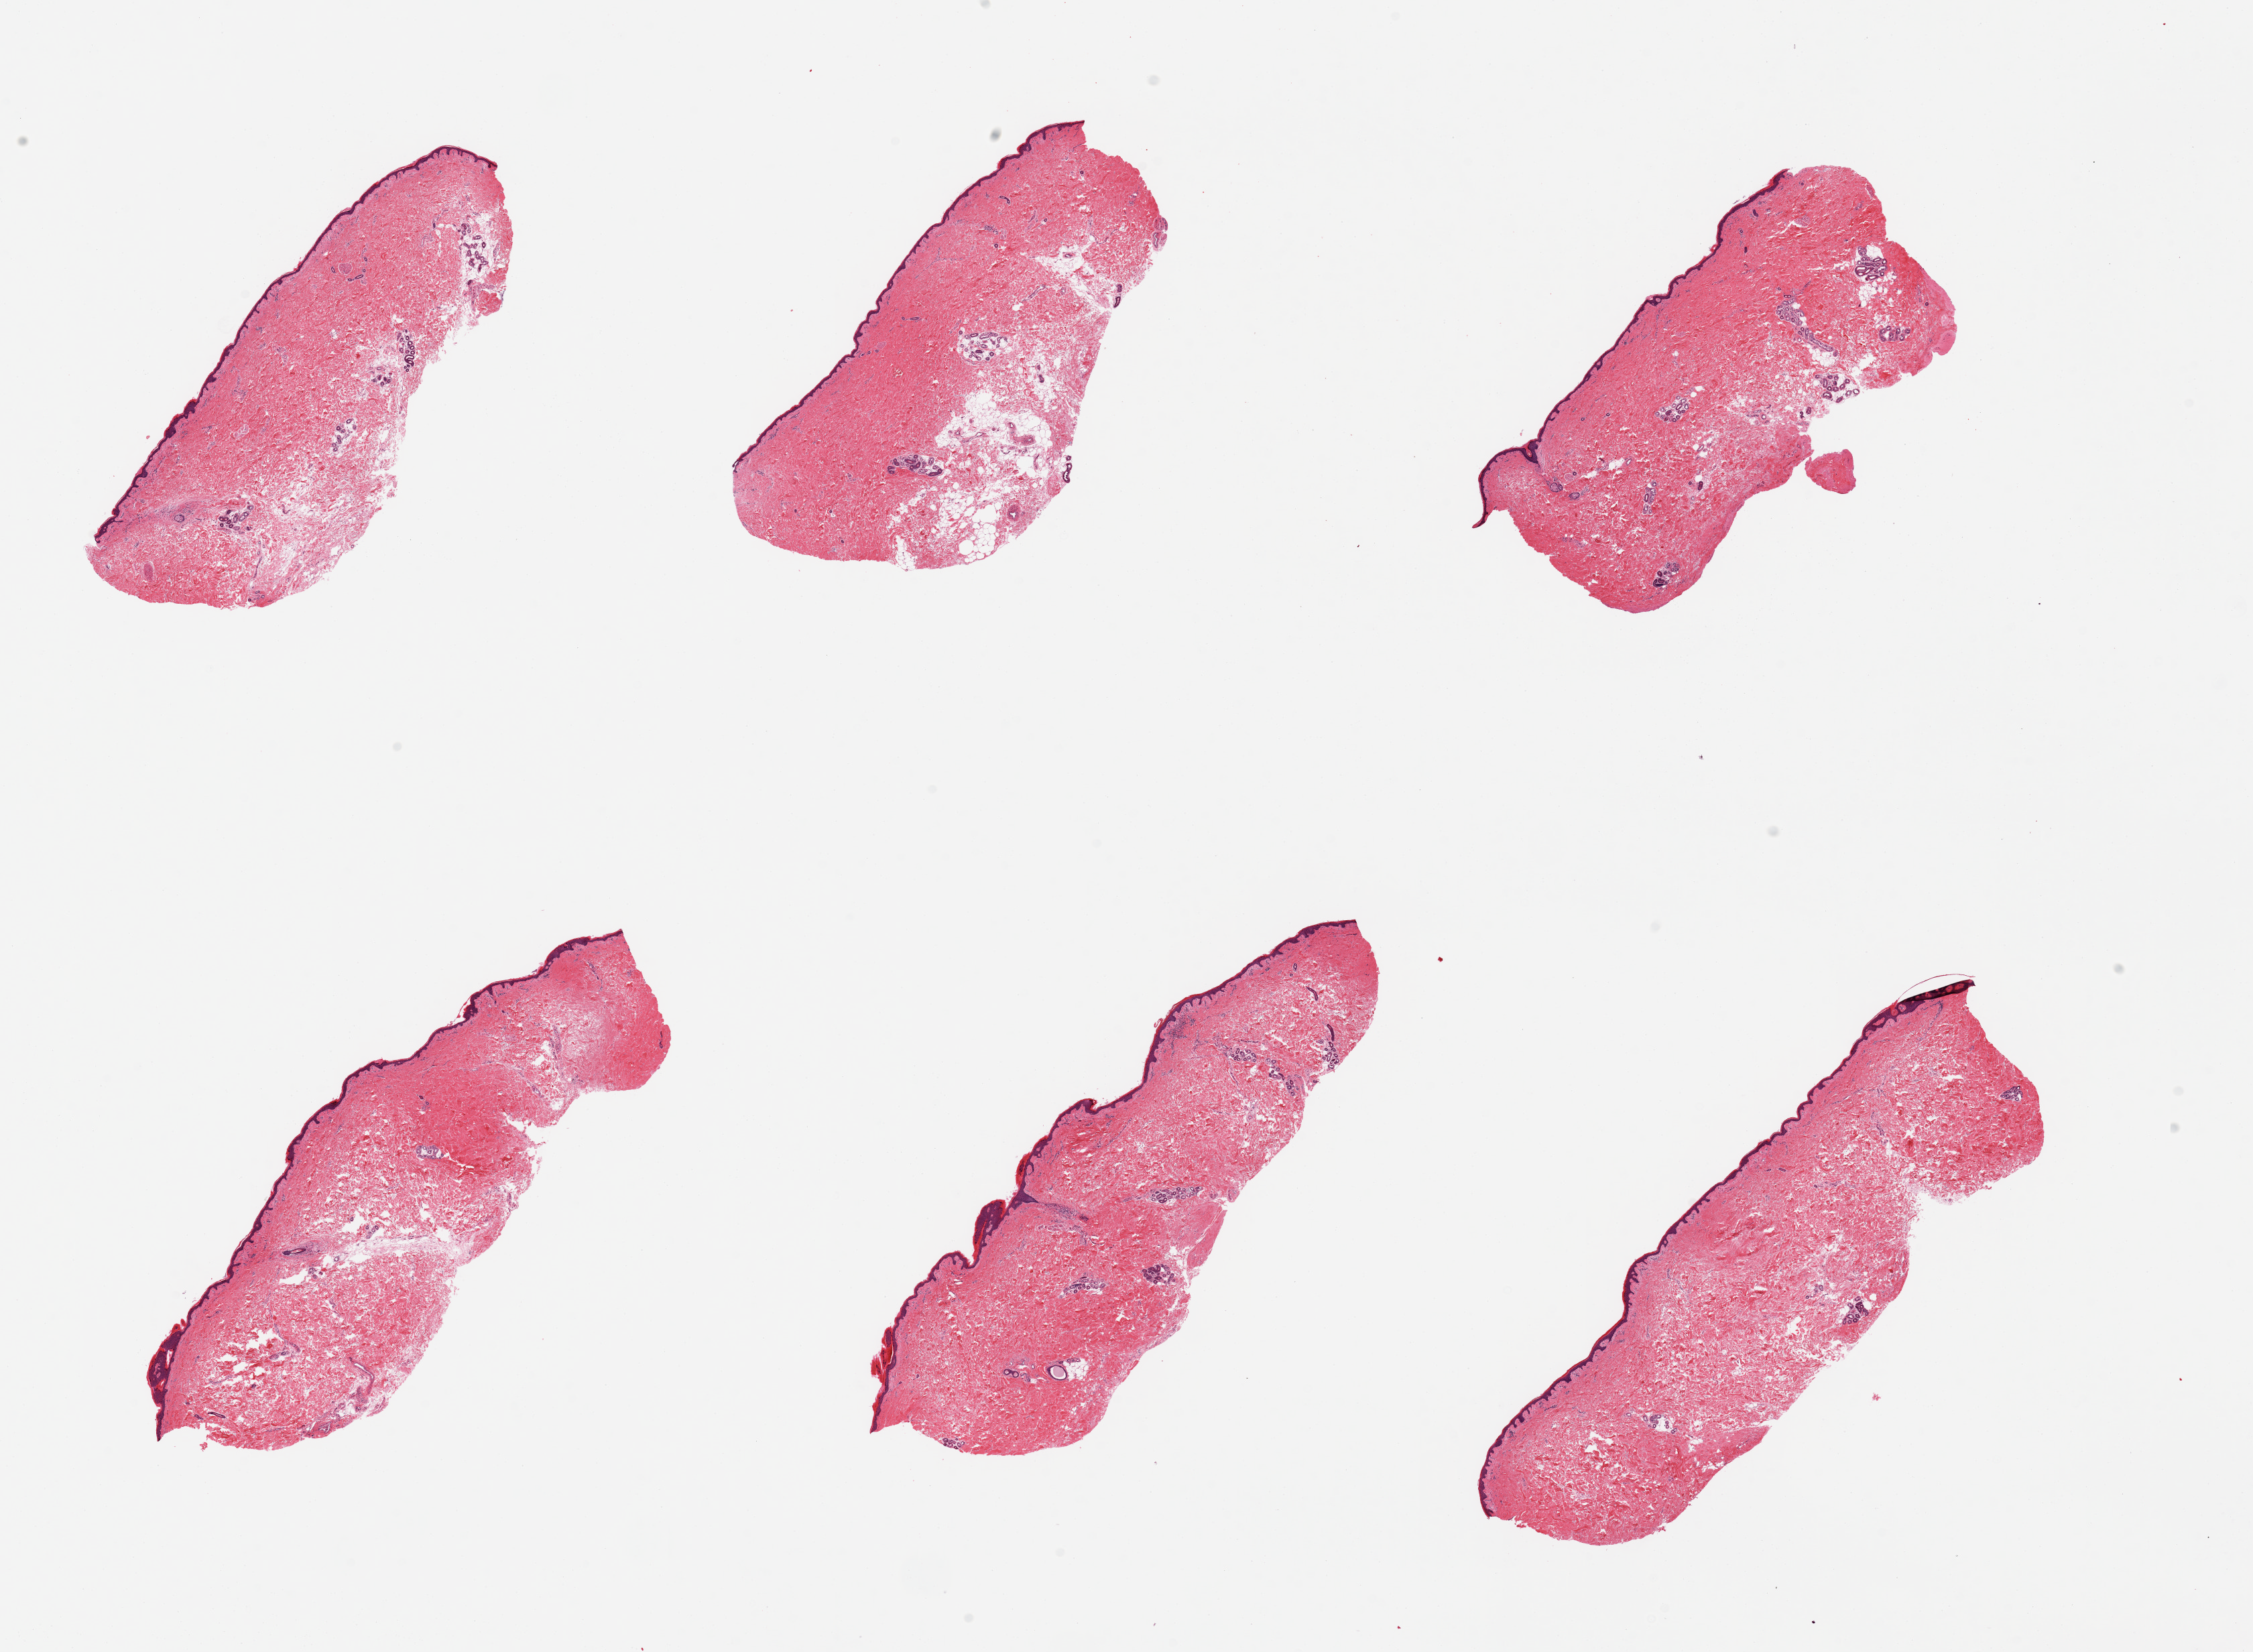
Digitized H&E-stained section, whole scanned area (about 26.6 x 19.5 mm, acquisition: 20x scan) shown as a low-resolution overview, PAXgene-fixed, paraffin-embedded tissue, sampled site (target tissue): skin of suprapubic region, donor tissue sample. Female donor.
- pathologist's review note for this sample: 6 pieces, minimal dermal fat, squamous epithelium is ~50 microns